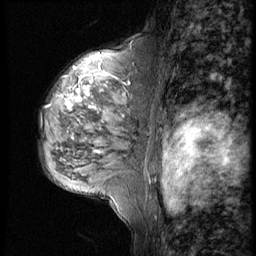
Breast MRI (dynamic contrast-enhanced), one sagittal slice; position 34 of 56 along the scan axis; 4 images stored at this slice position (order not interpretable as contrast timing); 1.5 T; TE 4.2 ms, TR 9 ms; 256 × 256 image matrix, field of view 180 × 180 mm. Patient: female, 50 years. From the clinical record (not read from this slice): setting: breast cancer imaged before/during neoadjuvant chemotherapy; receptor status: triple-negative.
Outlined on this slice (semi-automatic segmentation, software-assisted and operator-edited):
- analysis volume of interest (the breast-tissue region the enhancement analysis was run in; not a lesion): box from (x=38, y=46) to (x=148, y=188) px
- tumour enhancement mask (voxels above the 140 % enhancement threshold inside the analysis volume of interest): (x=49, y=87)–(x=103, y=155)